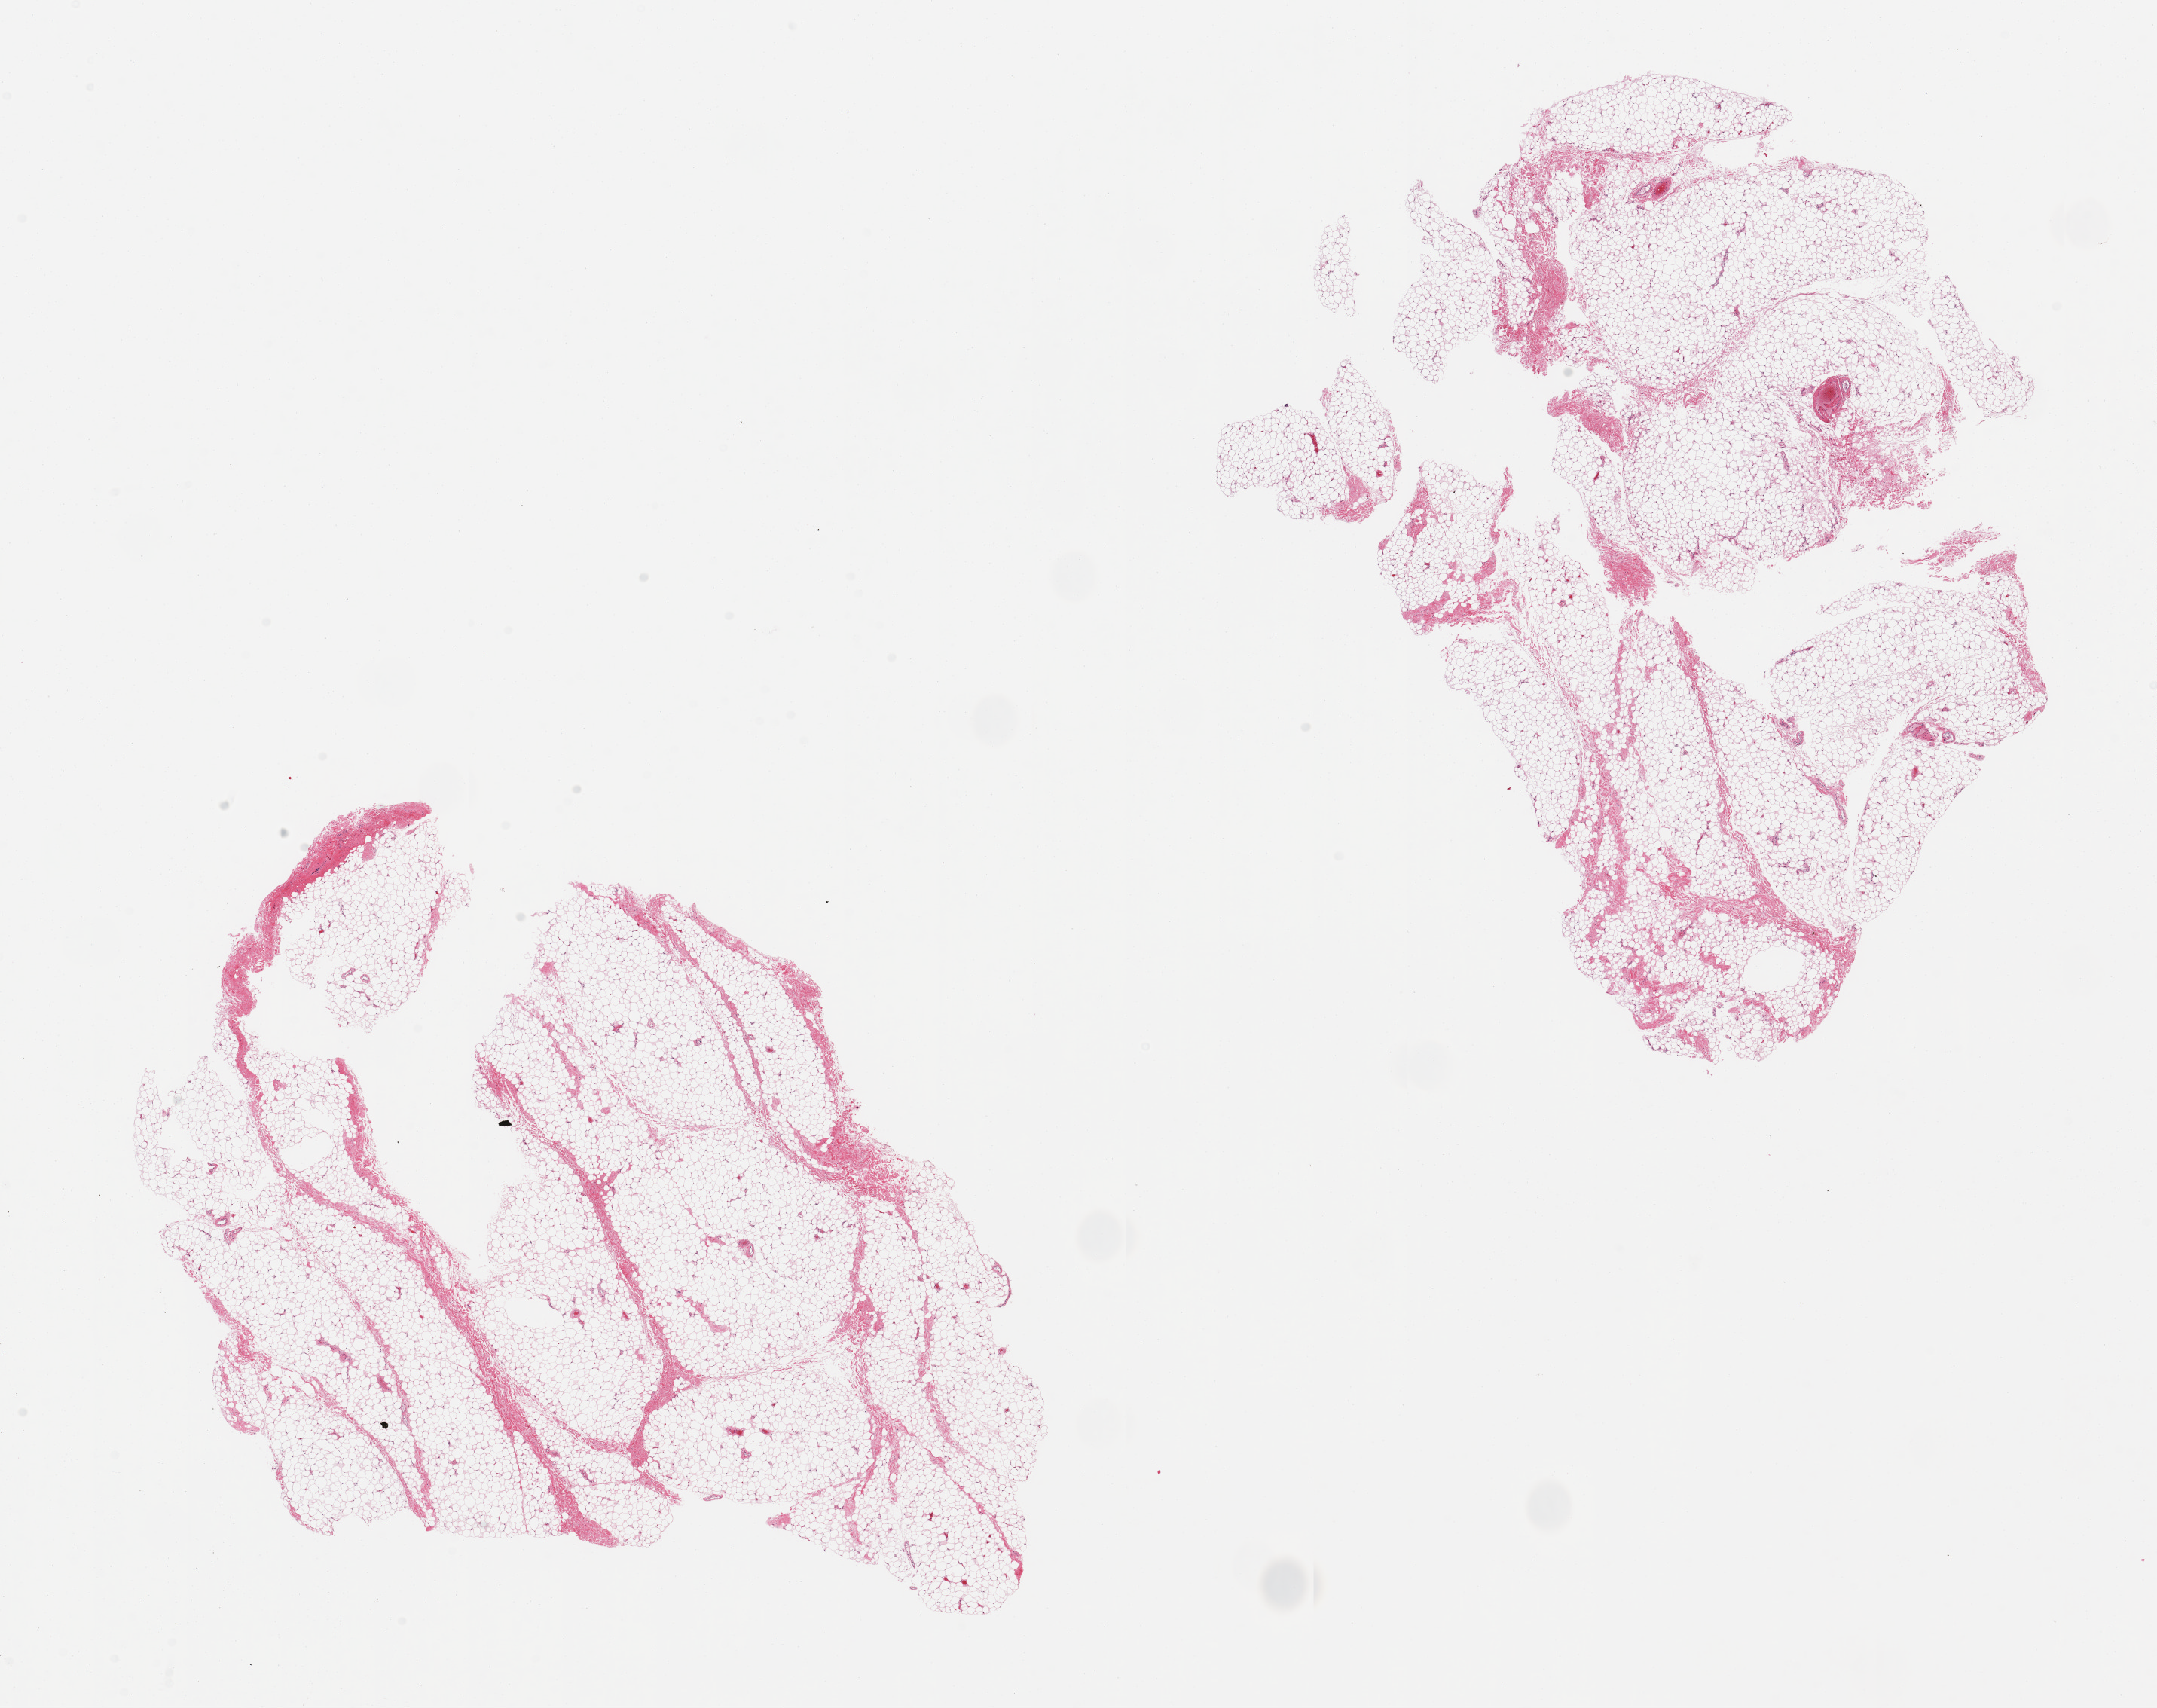
Haematoxylin and eosin whole-slide image — a low-resolution overview of the entire scanned area, about 22.6 x 17.9 mm, PAXgene-fixed, paraffin-embedded tissue, target tissue: breast, donor tissue sample. Donor sex: male.
Review note (as recorded): 2 pieces; fibroadipose tissue with no obvious mammary ducts.